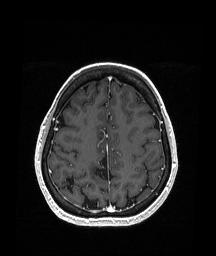
Brain MRI from a brain-tumour surgery series, one axial slice; slice 61 of 151 in the series (ordered by position); T1-weighted post-contrast; 1.05 mm slice thickness; 216 × 256 image matrix, field of view 211 × 250 mm. Case-level facts recorded for this patient, not image findings: histopathology: Oligodendroglioma; WHO grade: 2; IDH mutation: yes; tumour location: Right Parietal.
Annotated regions visible in this slice (manually delineated by an expert):
- previous resection cavity: box from (x=94, y=149) to (x=109, y=183) px